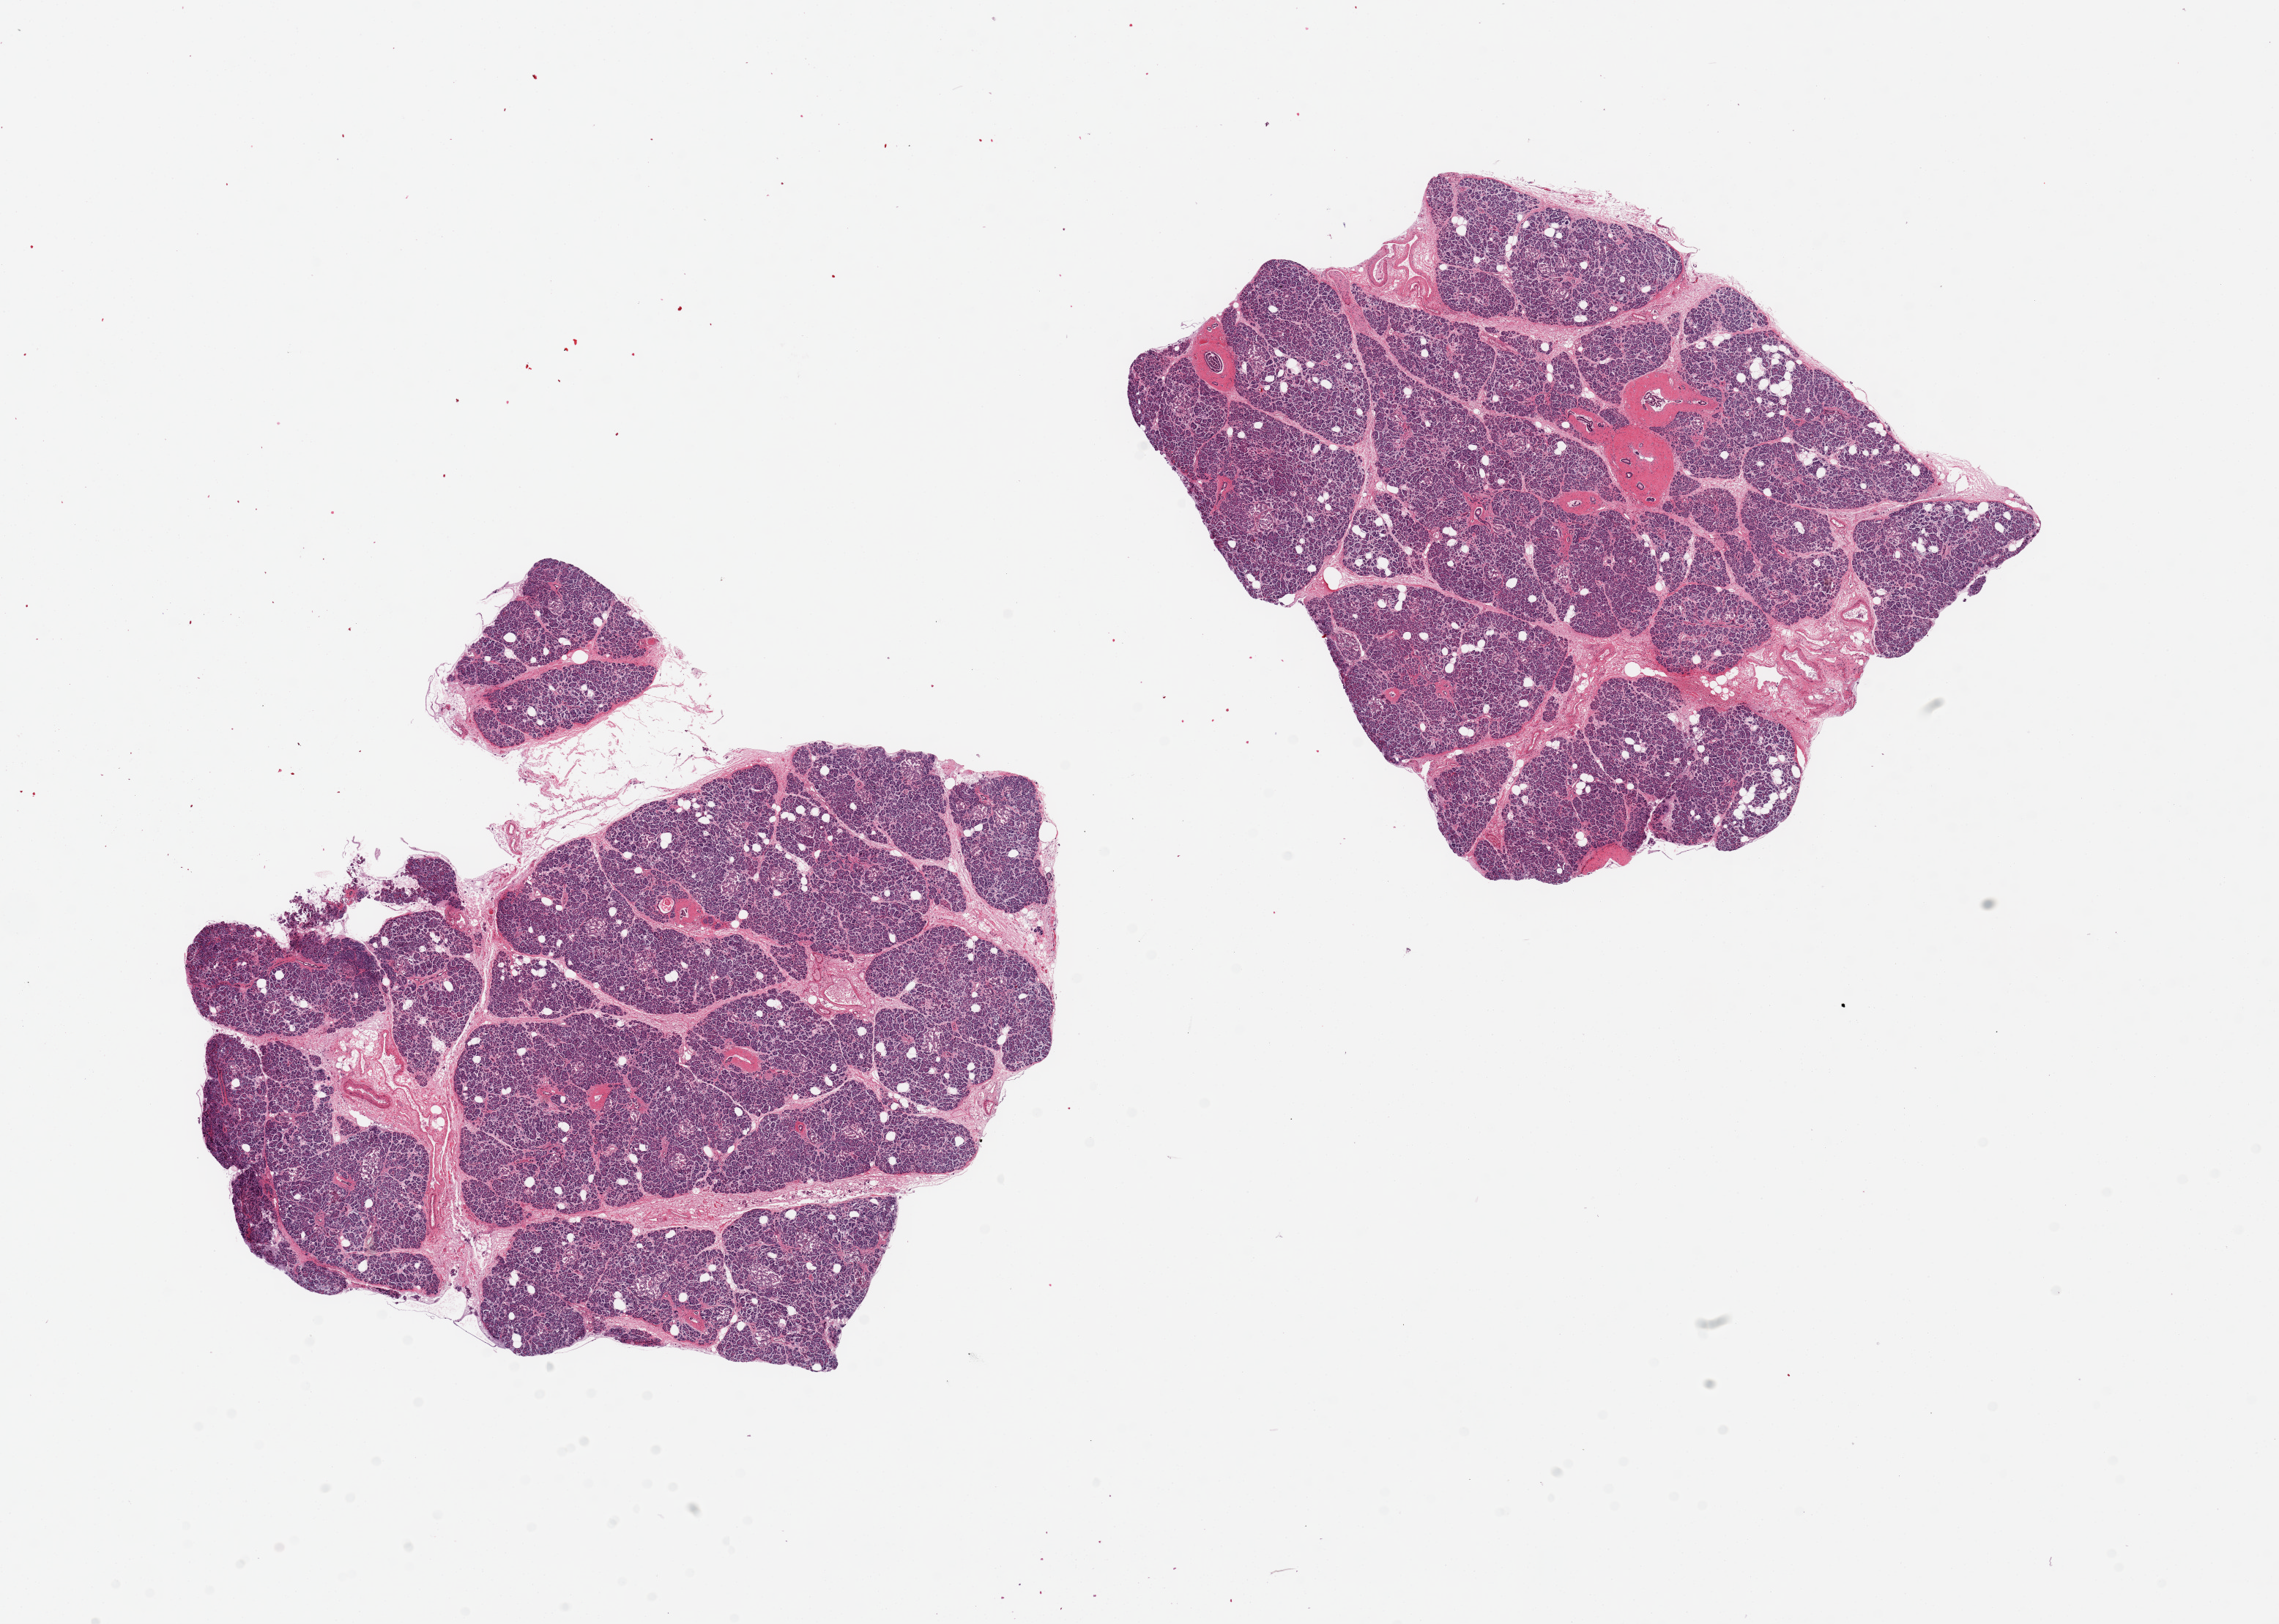
Hematoxylin and eosin (H&E) whole-slide image — a low-resolution overview of the entire scanned area, about 24.6 x 17.5 mm, PAXgene-fixed paraffin-embedded (PFPE) section, section of pancreas (target tissue), tissue donor sample. Donor sex: female.
Pathologist's review note for this sample: 2 pieces, 9.5x9 & 8x7mm; Well dissected.